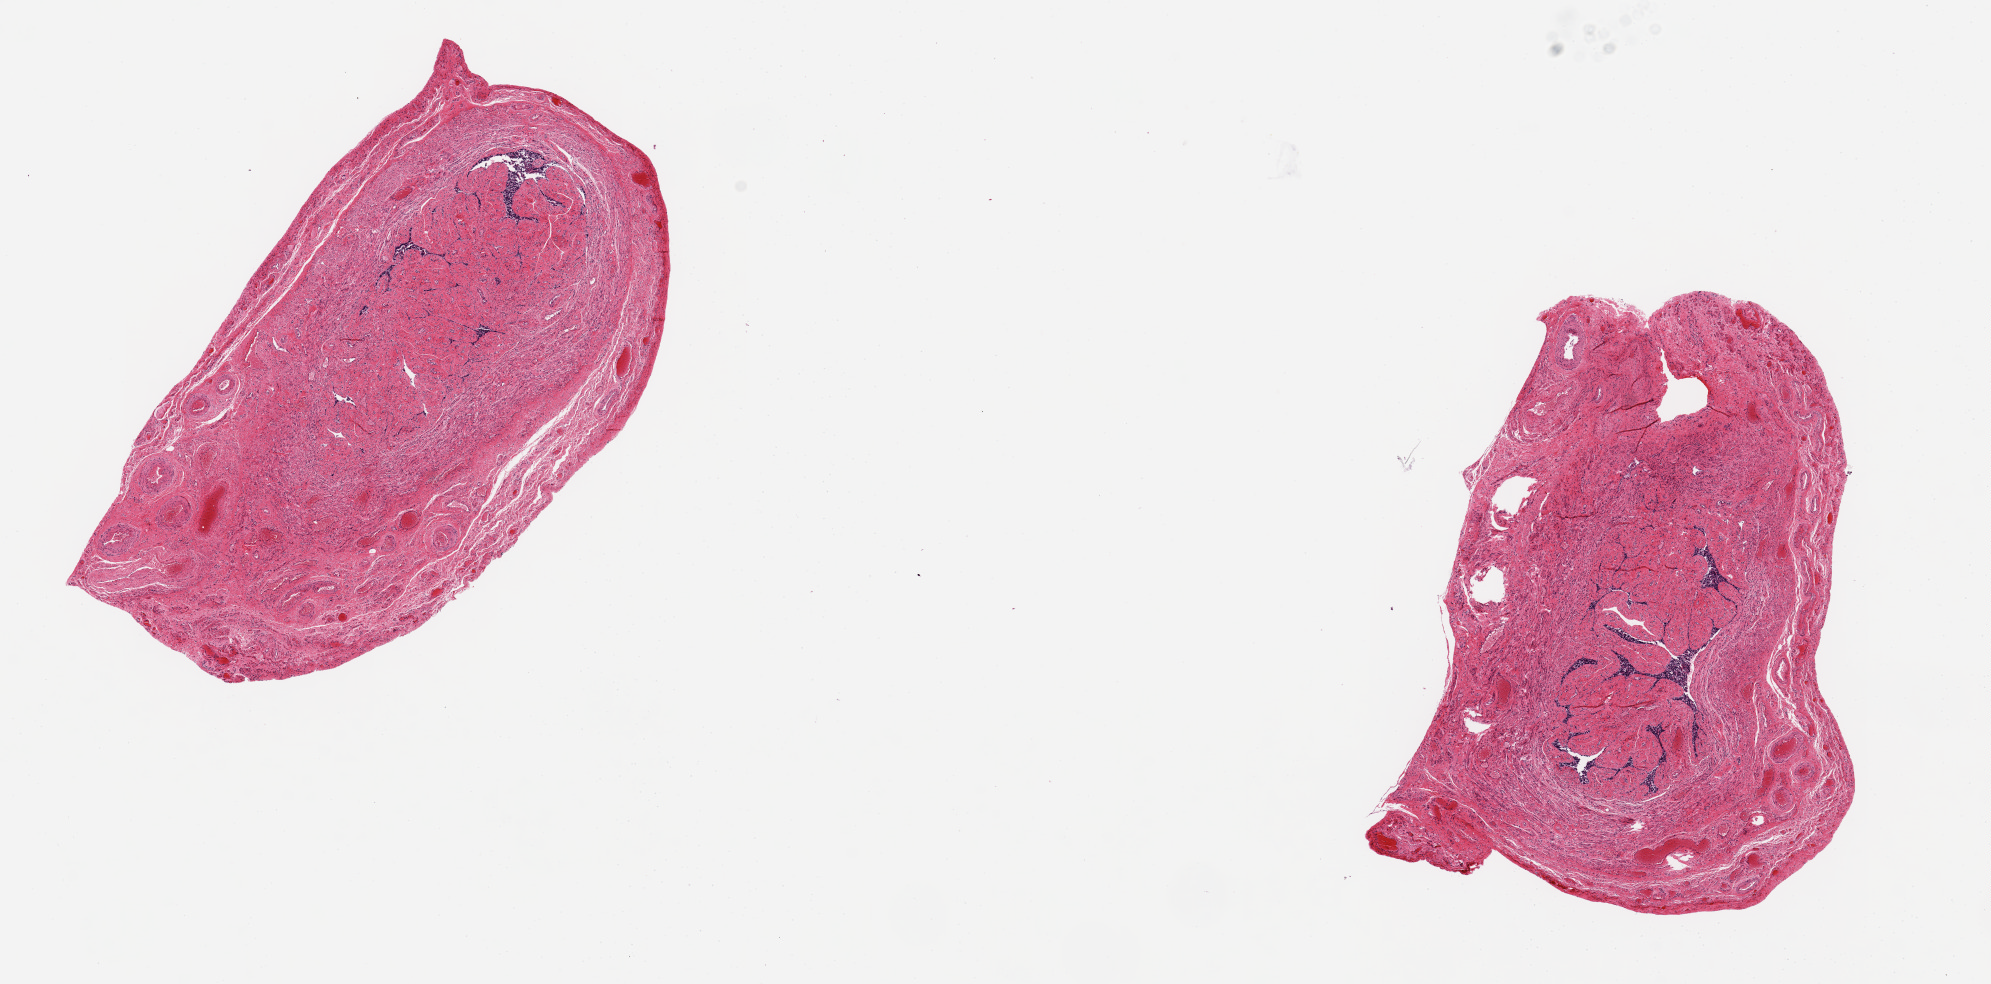
Digitized hematoxylin and eosin (H&E)-stained section — a low-resolution overview of the entire scanned area, about 15.8 x 7.8 mm; PAXgene-fixed paraffin-embedded (PFPE) section; target tissue: fallopian tube; tissue donor sample.
* review note (as recorded): 2 aliquots, ~5x3.5mm. Lining epithelium badly autolyzed